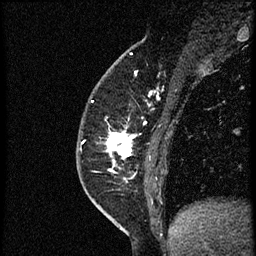
Breast MRI (dynamic contrast-enhanced), one sagittal slice; slice 20 of 56 in the series (ordered by position); dynamic contrast-enhanced study with each time point stored as its own series, time point 2 of 4 at this slice position (early post-contrast, ordered by acquisition time); 1.5 T; TE 4.2 ms, TR 18.9 ms; 2 mm slice thickness; 256 × 256 image matrix, field of view 200 × 200 mm. Female patient. Case-level facts recorded for this patient, not image findings: setting: breast cancer imaged before/during neoadjuvant chemotherapy; receptor status: HER2-positive.
Structures marked on this image (semi-automatic segmentation, software-assisted and operator-edited):
- analysis volume of interest (the breast-tissue region the enhancement analysis was run in; not a lesion): box from (x=105, y=92) to (x=172, y=189) px
- tumour enhancement mask (voxels above the 100 % enhancement threshold inside the analysis volume of interest): (x=107, y=132)–(x=136, y=171)